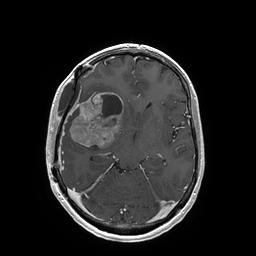
Brain MRI from a brain-tumour surgery series, one axial slice. Slice 98 of 202 in the series (ordered by position). T1-weighted post-contrast. 1 mm slice thickness. 256 × 256 image matrix, field of view 250 × 250 mm. Case-level facts recorded for this patient, not image findings: histopathology: Glioblastoma; WHO grade: 4; IDH mutation: no; tumour location: Right Insular.
Outlined on this slice (manually delineated by an expert):
- tumour: bounding box (x1, y1, x2, y2) in pixels: (69, 92, 122, 149)